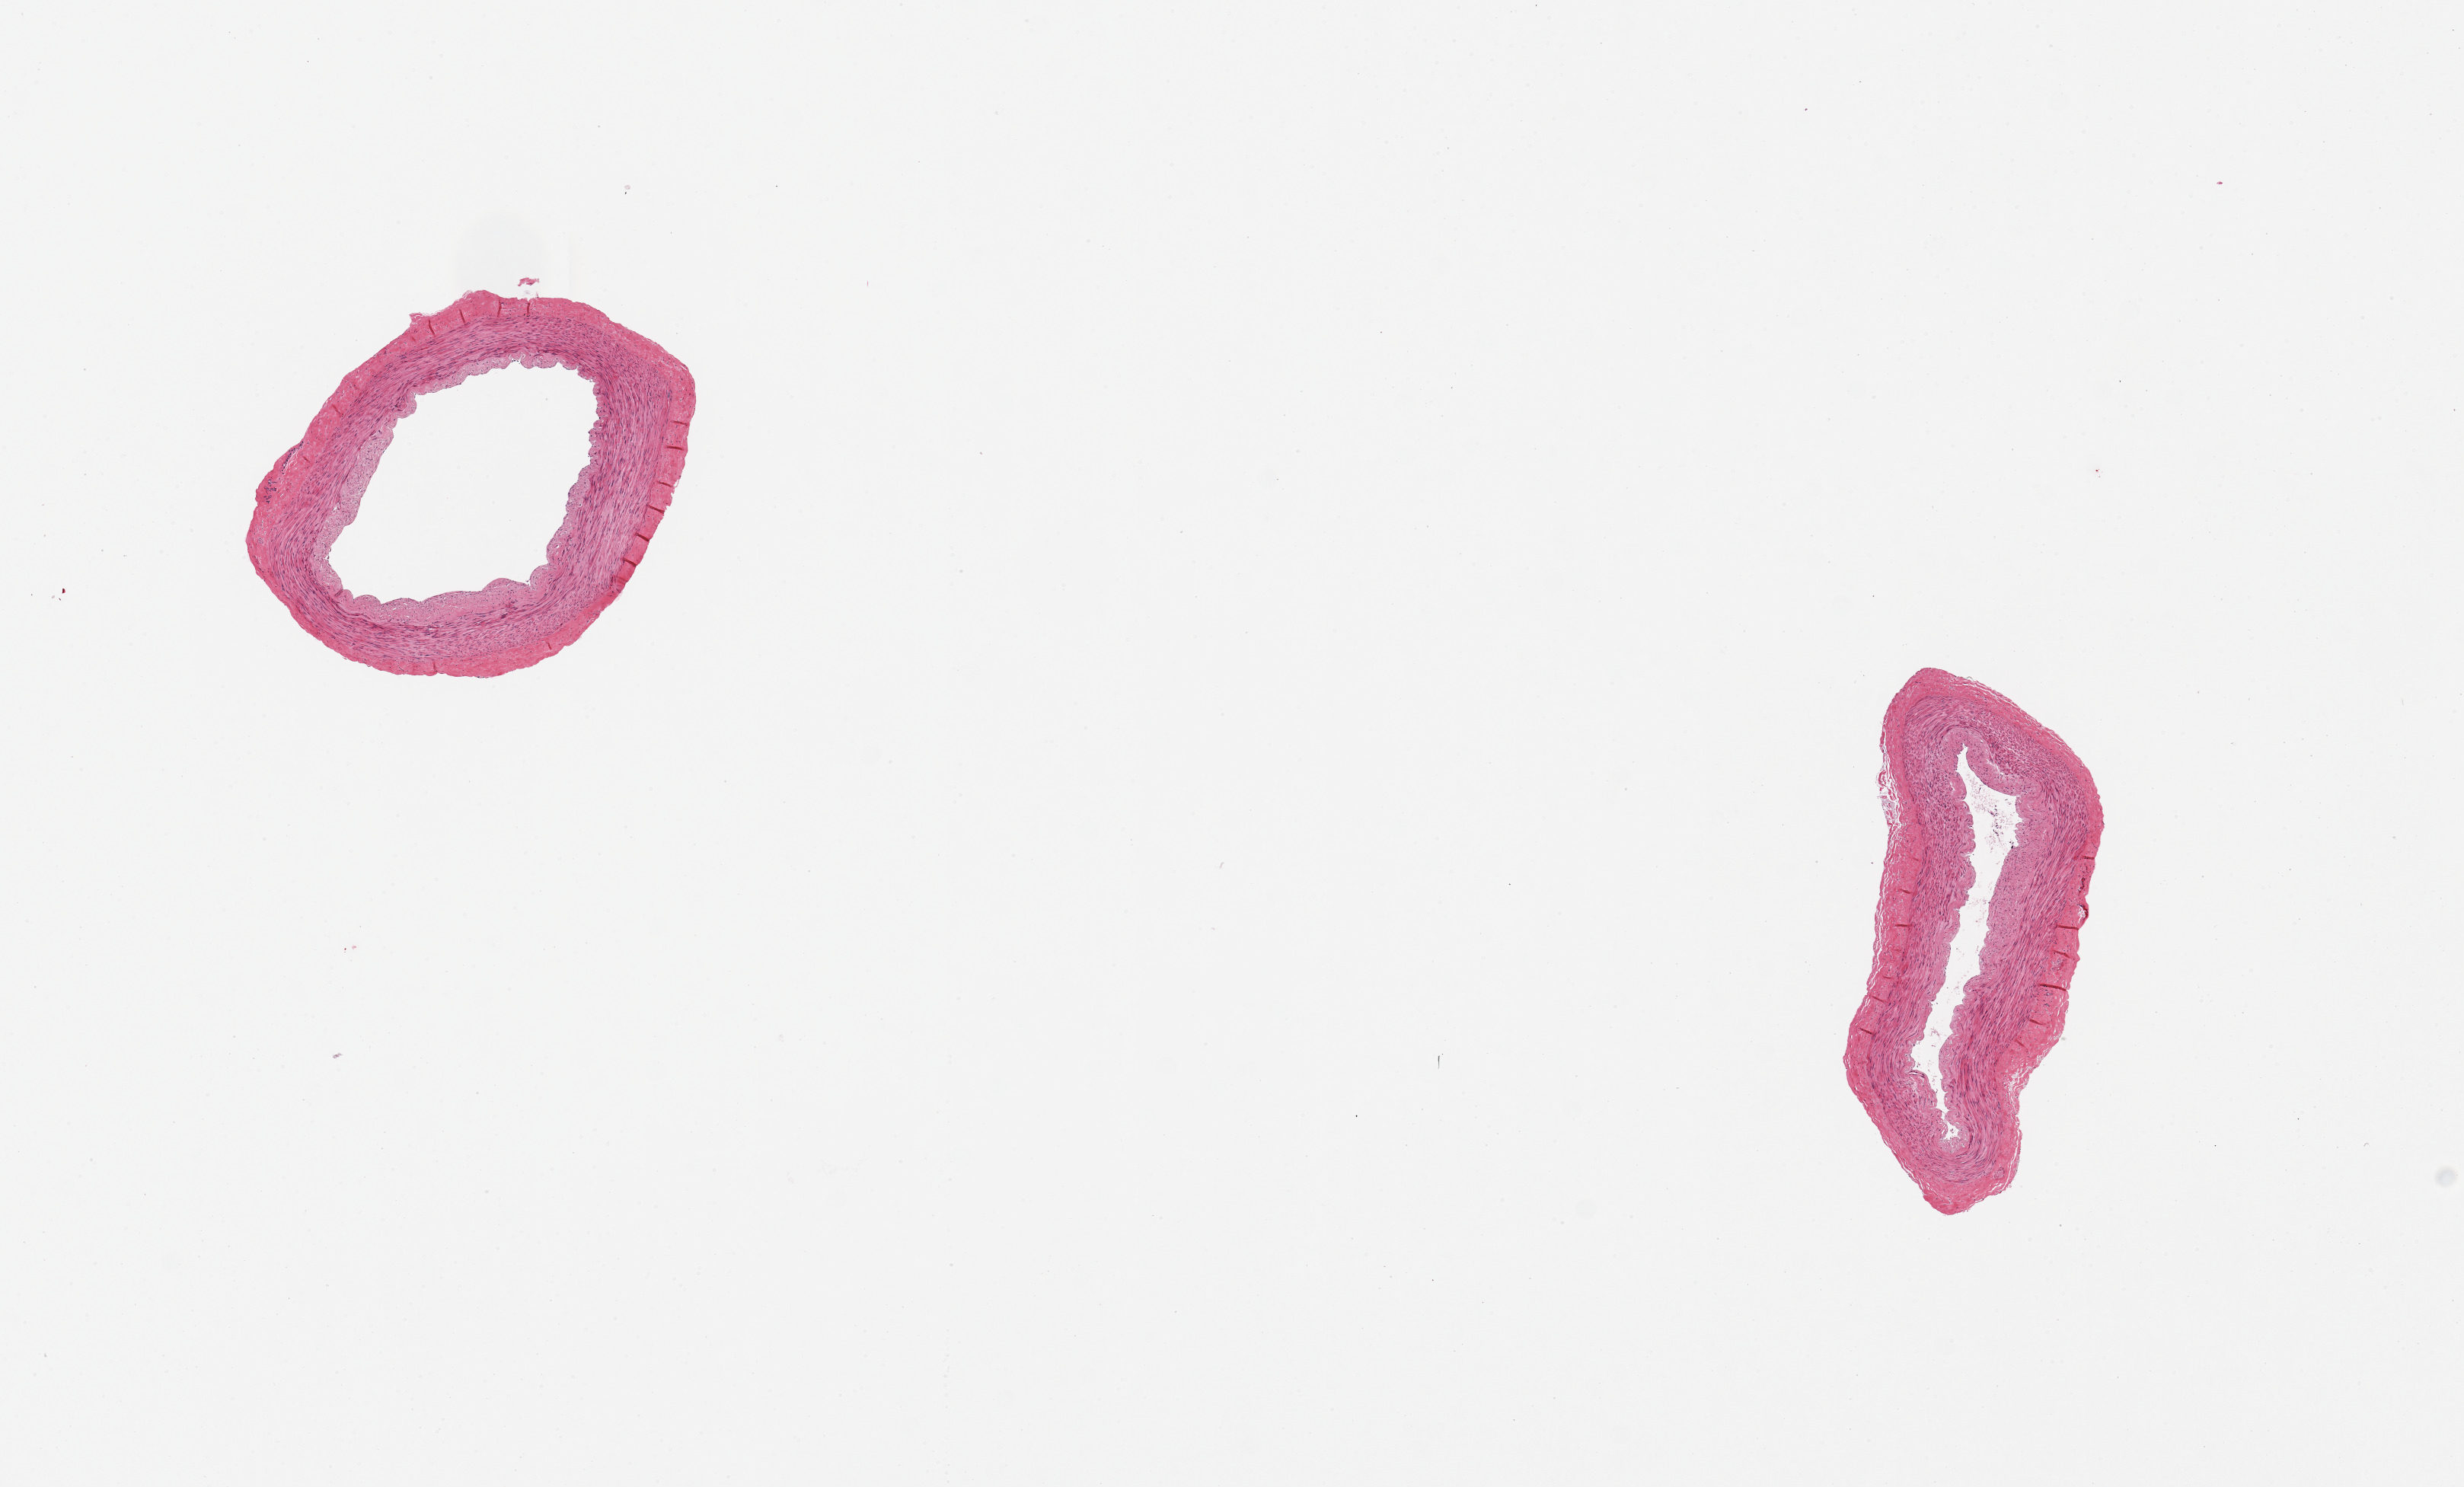
Whole-slide image, haematoxylin and eosin stain — whole scanned area (about 12.8 x 7.7 mm) shown as a low-resolution overview. PAXgene-fixed, paraffin-embedded tissue. Target tissue: tibial artery. Donor tissue sample. Donor: male.
• reviewer comment on this tissue sample: 2 pieces. Well trimmed. Minimal intimal thickening